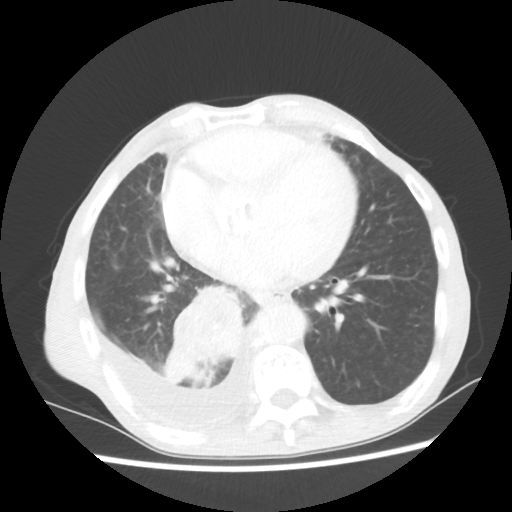
Chest CT, one axial slice; slice 24 of 60 in the series (ordered by position); reconstruction kernel STANDARD; lung window (W 1500 / L -600 HU); 5 mm slice thickness; 512 × 512 image matrix, field of view 335 × 335 mm. Male patient, age 76 years. Case-level facts recorded for this patient, not image findings: clinical TNM (as recorded): T3 N3 M1a; histopathological grade: G3.
Annotated regions visible in this slice (rectangle marked by the reading radiologist):
- lung tumour (recorded histology: squamous cell carcinoma): bounding box (x1, y1, x2, y2) in pixels: (161, 282, 248, 386)